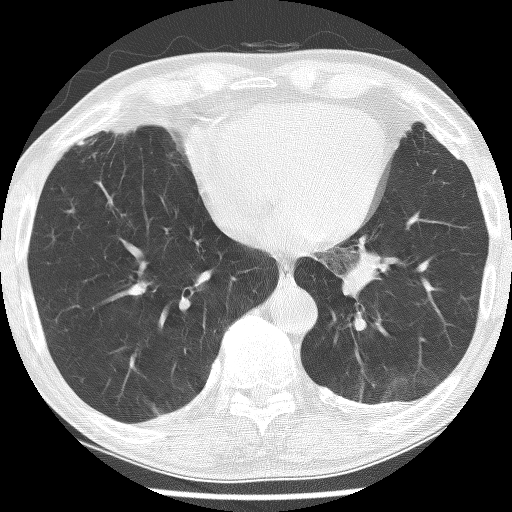
Low-dose screening chest CT, axial slice, baseline screening round, lung window (W 1500 / L -600 HU), 120 kVp, 512 × 512 image matrix. Male, age 74 years at enrolment. Current smoker at enrolment.
• Expert reader's lesion annotation, bounding box <318,230,426,324> (left, top, right, bottom; pixels).
• Screening reader's record for this exam (one nodule recorded; not confirmed to be the boxed lesion): non-calcified nodule or mass ≥4 mm, left lower lobe, 30 × 27 mm, spiculated (stellate) margins, soft tissue attenuation.
• Participant outcome: lung cancer diagnosed 151 days after this screen — adenocarcinoma, NOS, left lower lobe, stage IIIA (AJCC 6th edition), 49 mm at pathology.